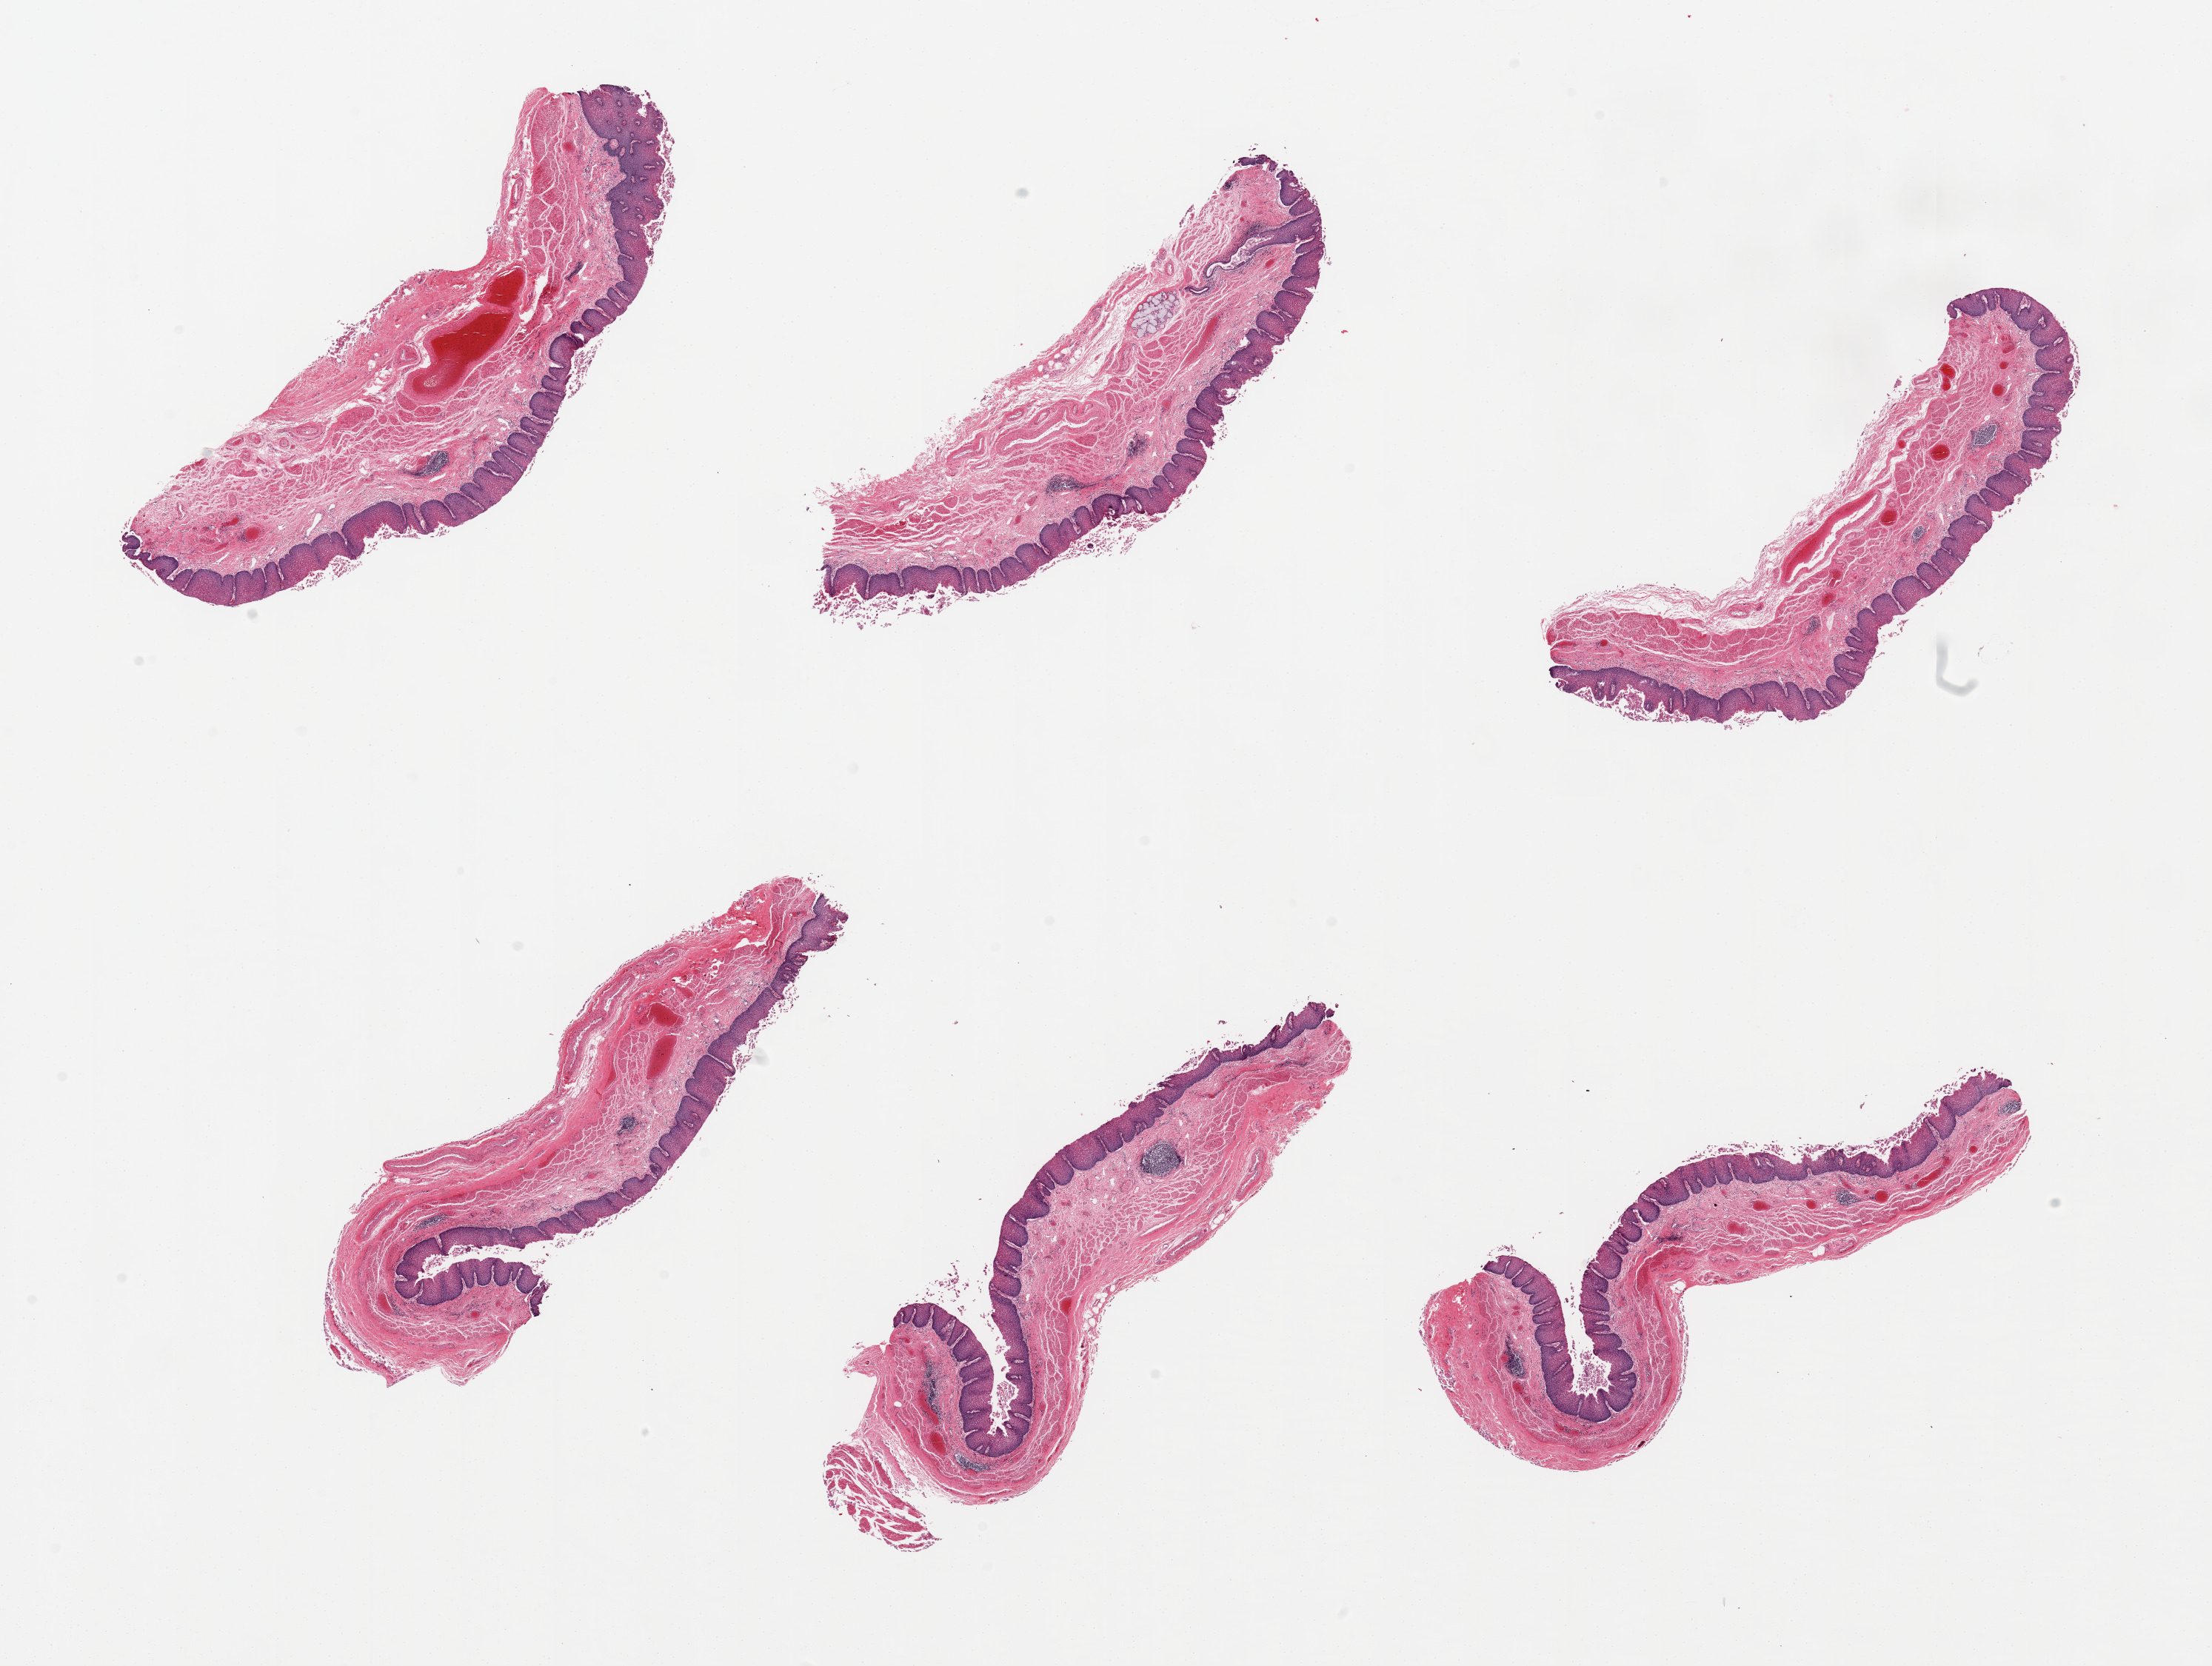
Digitized hematoxylin and eosin (H&E)-stained section — low-resolution overview of the scanned area, about 23.6 x 17.8 mm, PAXgene-fixed paraffin-embedded (PFPE) section, sampled site (target tissue): esophageal mucous membrane, tissue donor sample. Donor sex: male.
• review note (as recorded): 6 pieces; mucosa with partial epithelial sloughing, small portion of muscularis propria